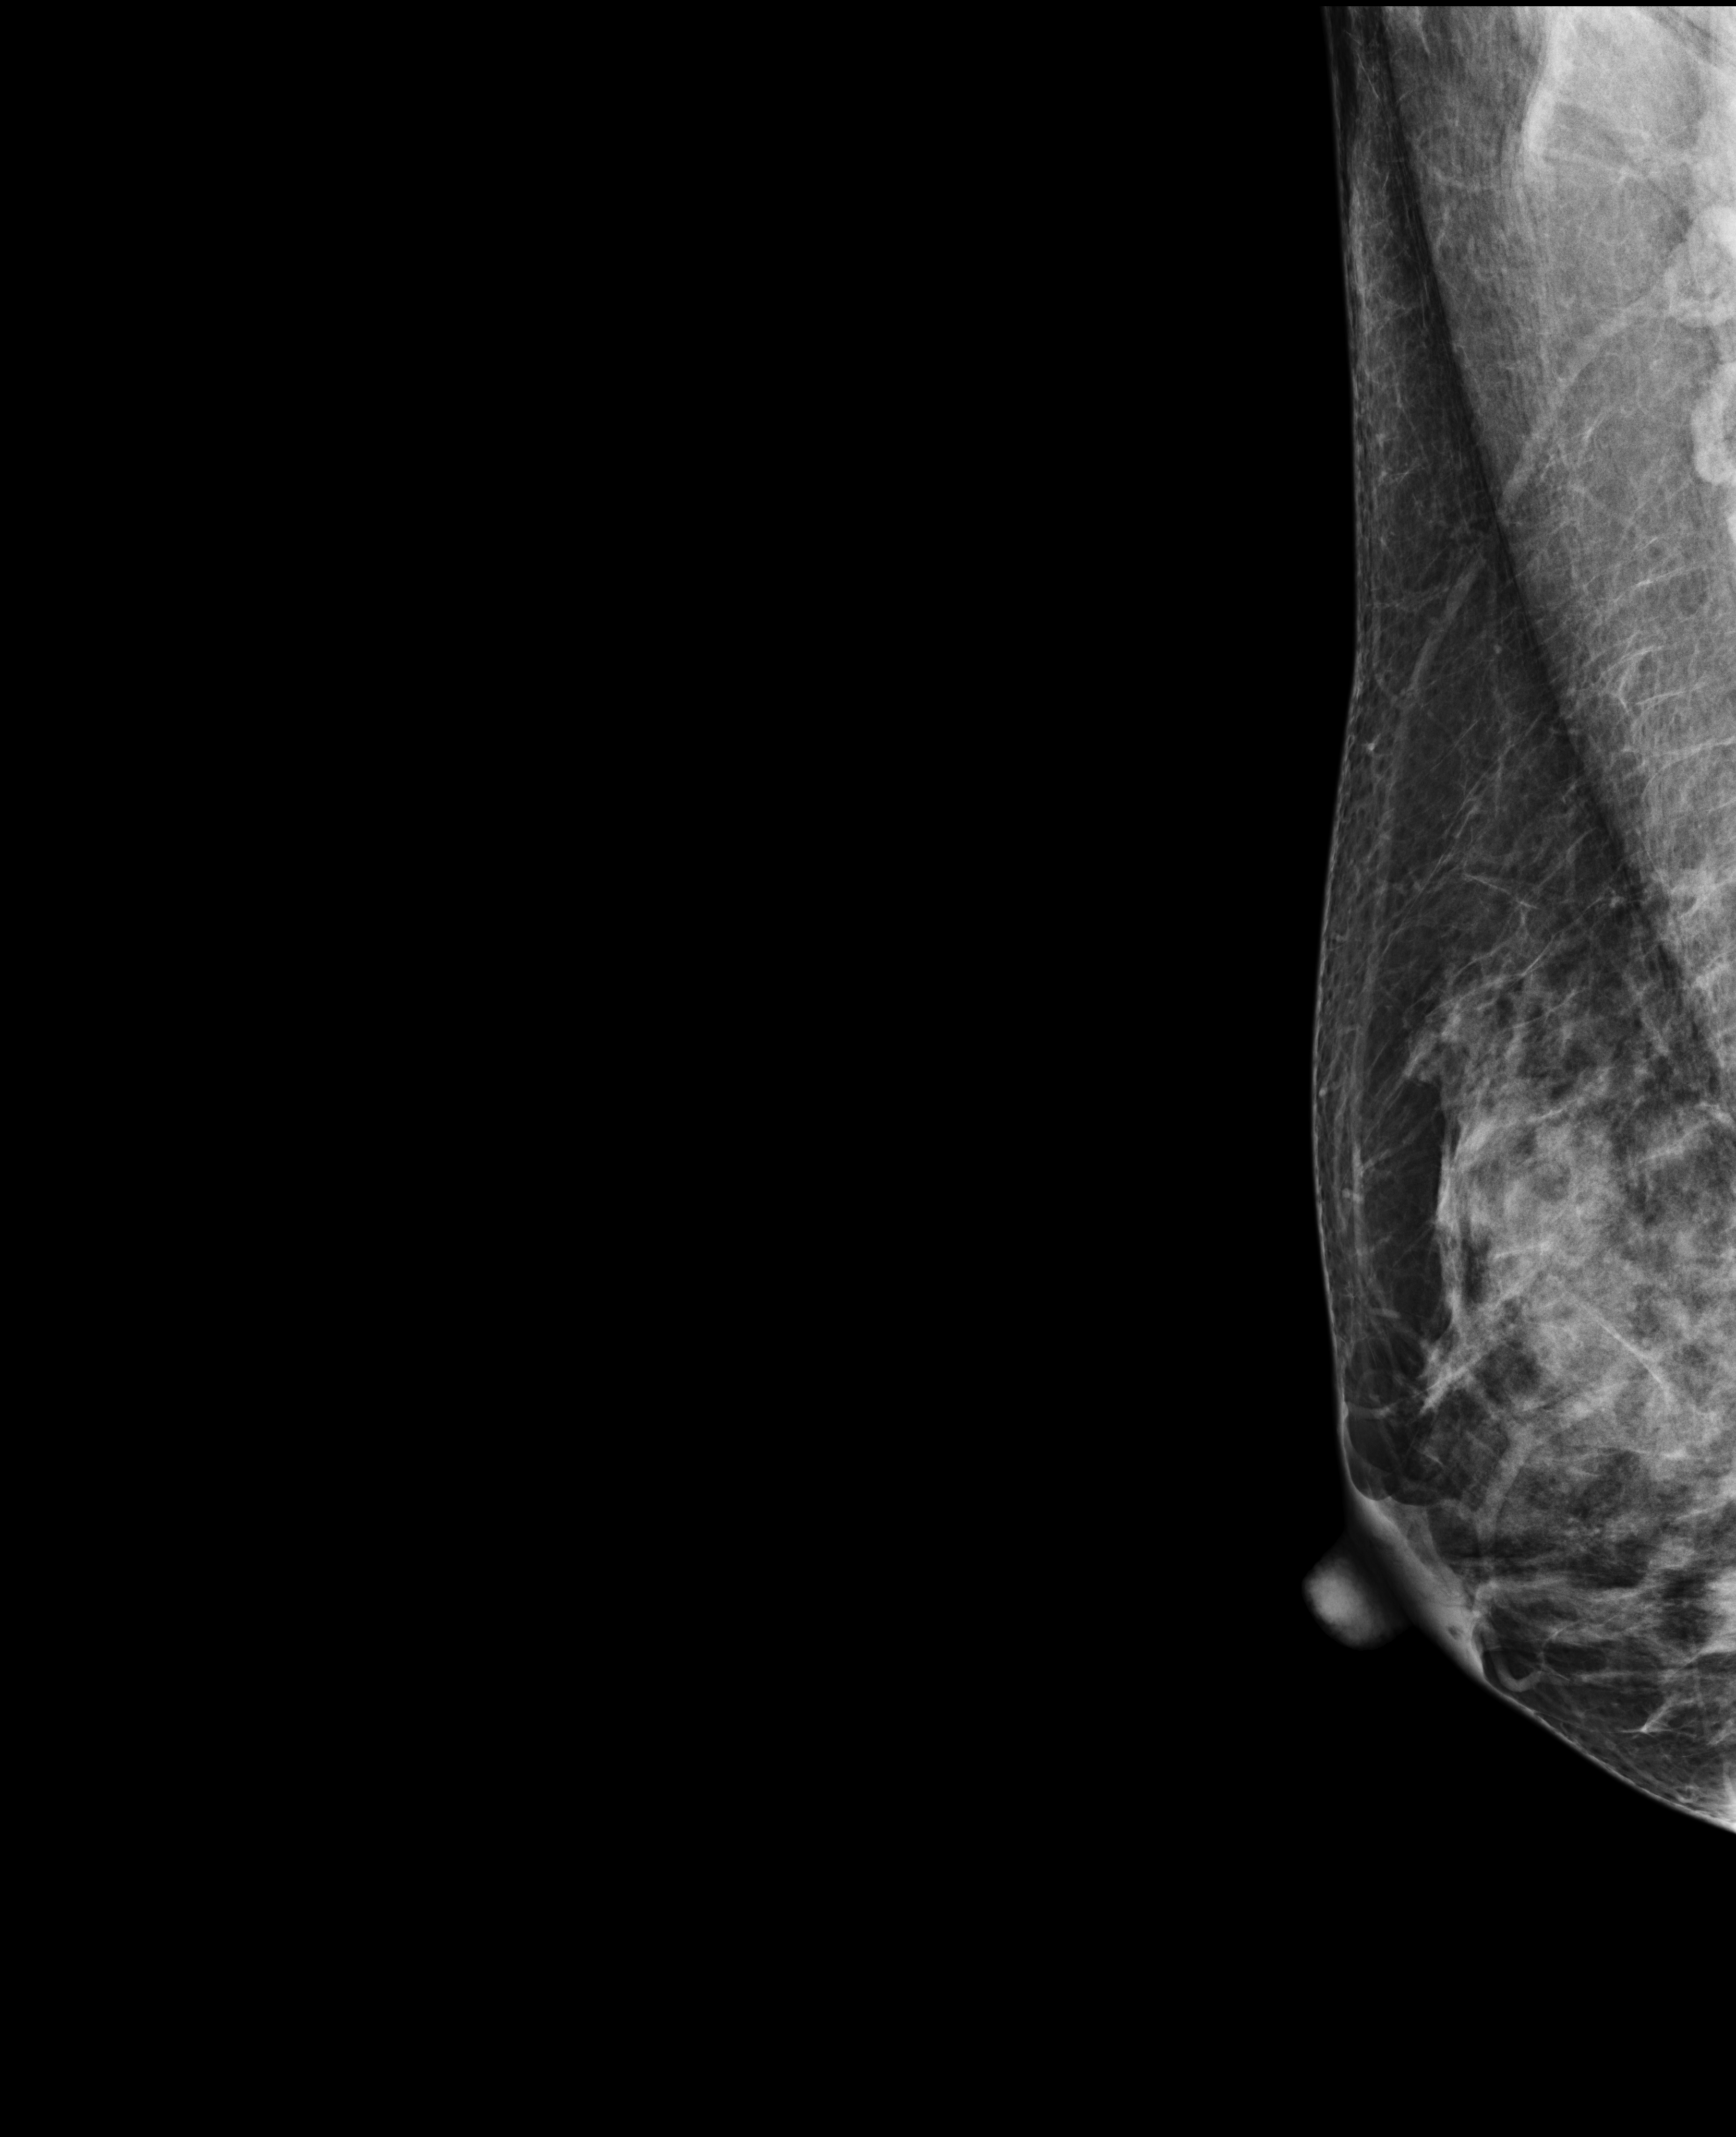
Annual screening mammography examination, compressed breast thickness 66 mm. Patient aged 42 years (female).
Image type: full-field digital mammogram. Breast: right. Projection: exaggerated CC view (lateral).